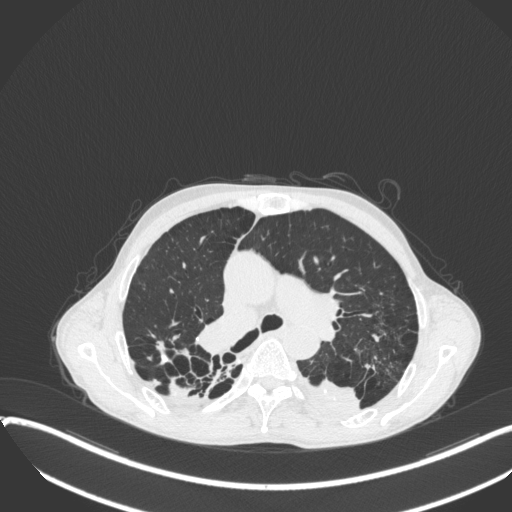
Chest CT, one axial slice. Position 248 of 400 along the scan axis. Reconstruction kernel B31f. Lung window (W 1500 / L -600 HU). 1 mm slice thickness. 512 × 512 image matrix. Patient: male, 57 years. From the clinical record (not read from this slice): clinical TNM (as recorded): T4 N0 M0.
Annotated regions visible in this slice (bounding box drawn by a radiologist):
- lung tumour (recorded histology: squamous cell carcinoma): bounding box [x1, y1, x2, y2] px = [297, 374, 362, 418]